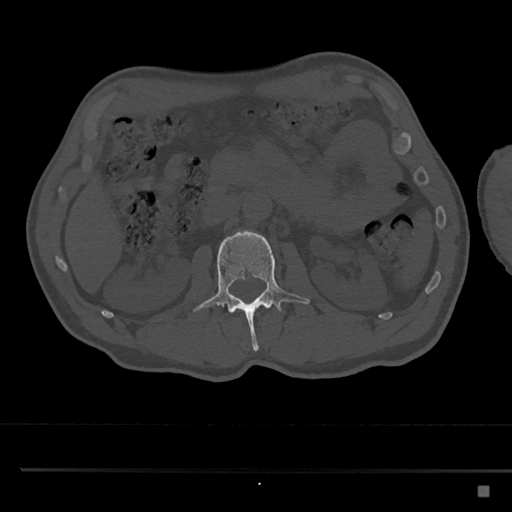
CT including the spine, one axial slice. Slice 763 of 797 in the series (ordered by position). Reconstruction kernel Br40s/3. 120 kVp. Bone window (W 1800 / L 400 HU). 0.5 mm slice thickness. 512 × 512 image matrix, field of view 391 × 391 mm. Patient: male, 59 years. From the clinical record (not read from this slice): primary cancer: prostate.
Structures marked on this image (semi-automatic segmentation, software-assisted and operator-edited):
- L2 vertebra: bounding box <193,230,310,352> (left, top, right, bottom; pixels)